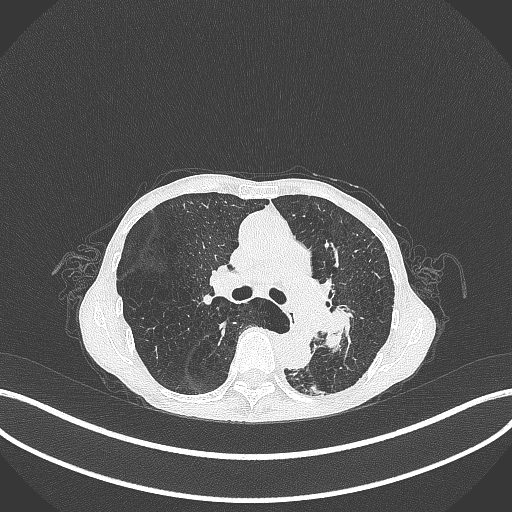
Chest CT, one axial slice; position 173 of 347 along the scan axis; reconstruction kernel B70f; 120 kVp; lung window (W 1500 / L -600 HU); 1 mm slice thickness; 512 × 512 image matrix, field of view 400 × 400 mm. Female patient, age 70 years. From the clinical record (not read from this slice): clinical TNM (as recorded): T3 N0 M0; histopathological grade: G3.
Outlined on this slice (rectangle marked by the reading radiologist):
- lung tumour (recorded histology: small cell carcinoma): box from (x=324, y=304) to (x=364, y=352) px